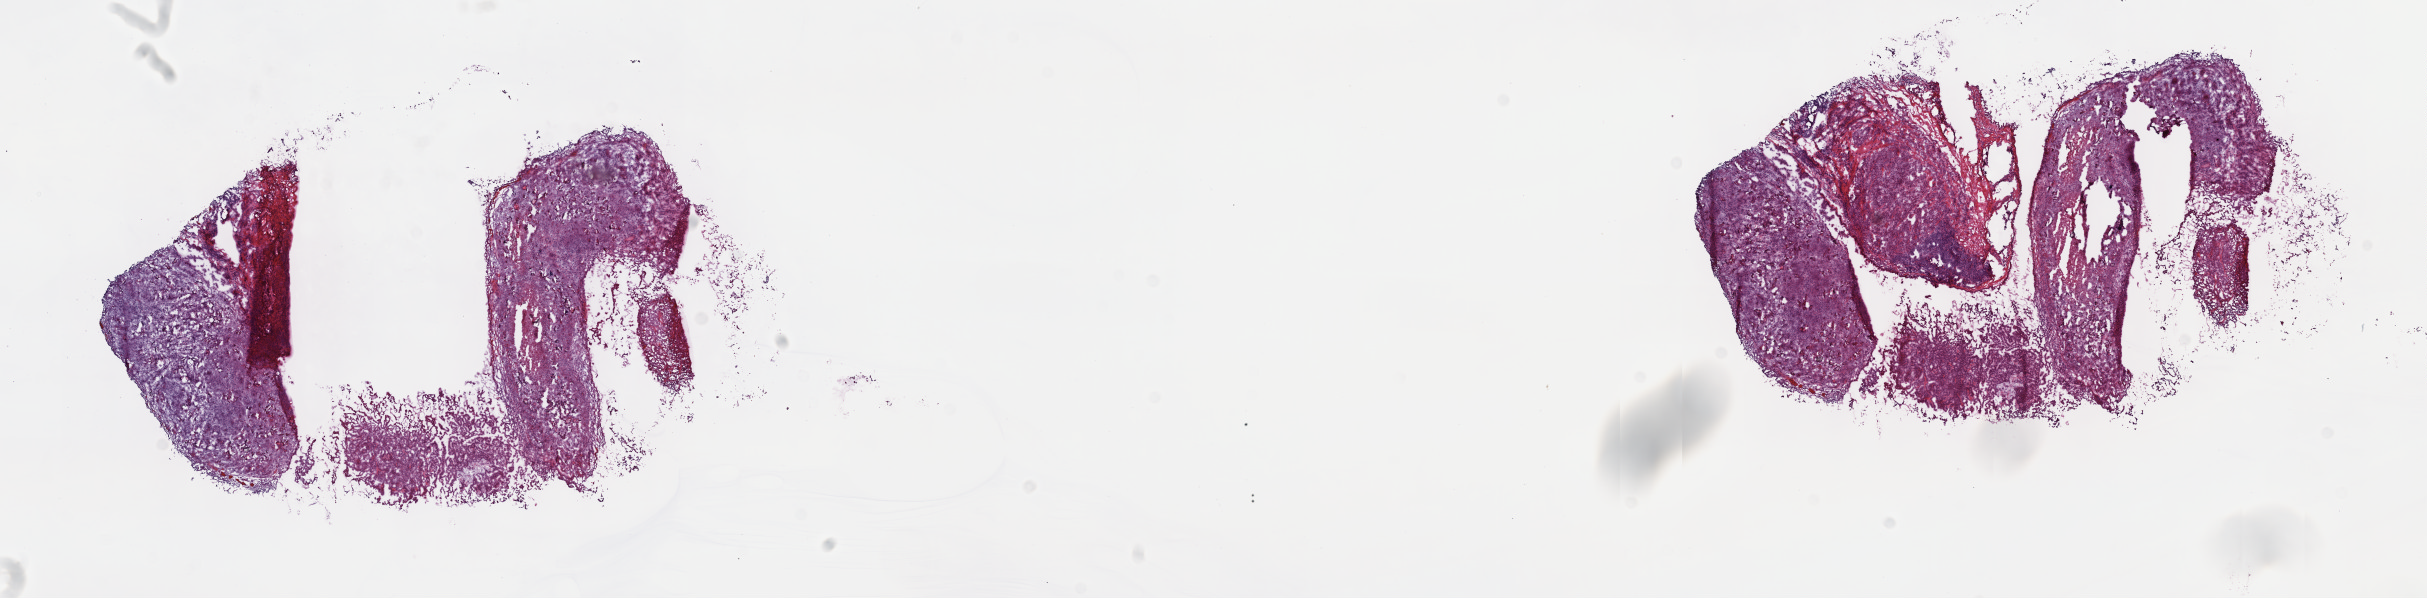
Digitized H&E-stained tissue section (whole slide), whole scanned area (about 19.6 x 4.8 mm, from a 40x scan) shown as a low-resolution overview, frozen section from the top of the tissue portion, sample: primary tumour, mesothelium. Male, age 64 years at initial diagnosis. Slide review estimates, as recorded: tumour cells 70%, tumour nuclei 70%, normal cells 0%, stromal cells 30%, necrosis 0%. Inflammatory infiltration, as recorded: lymphocyte infiltration 40%, monocyte infiltration 20%, neutrophil infiltration 20%.
Pathologic diagnosis: Mesothelioma, malignant. Laterality: right. AJCC pathologic stage: II (6th edition).